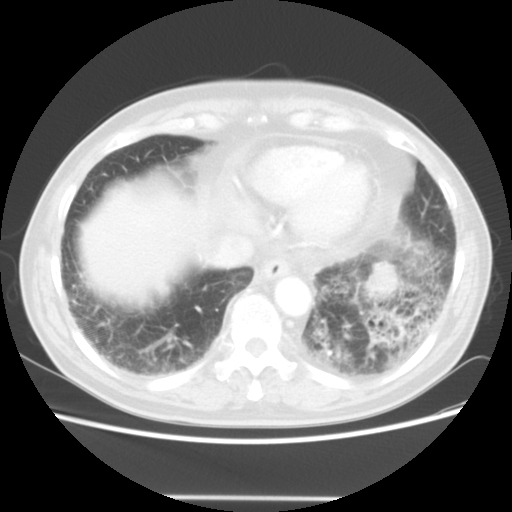
Chest CT, one axial slice; slice 12 of 56 in the series (ordered by position); reconstruction kernel STANDARD; 140 kVp; lung window (W 1500 / L -600 HU); 512 × 512 image matrix, field of view 360 × 360 mm. Patient: male, 66 years. Case-level facts recorded for this patient, not image findings: clinical TNM (as recorded): T4 N3 M0; histopathological grade: G3.
Structures marked on this image (rectangle marked by the reading radiologist):
- lung tumour (recorded histology: small cell carcinoma): bounding box <357,251,408,307> (left, top, right, bottom; pixels)